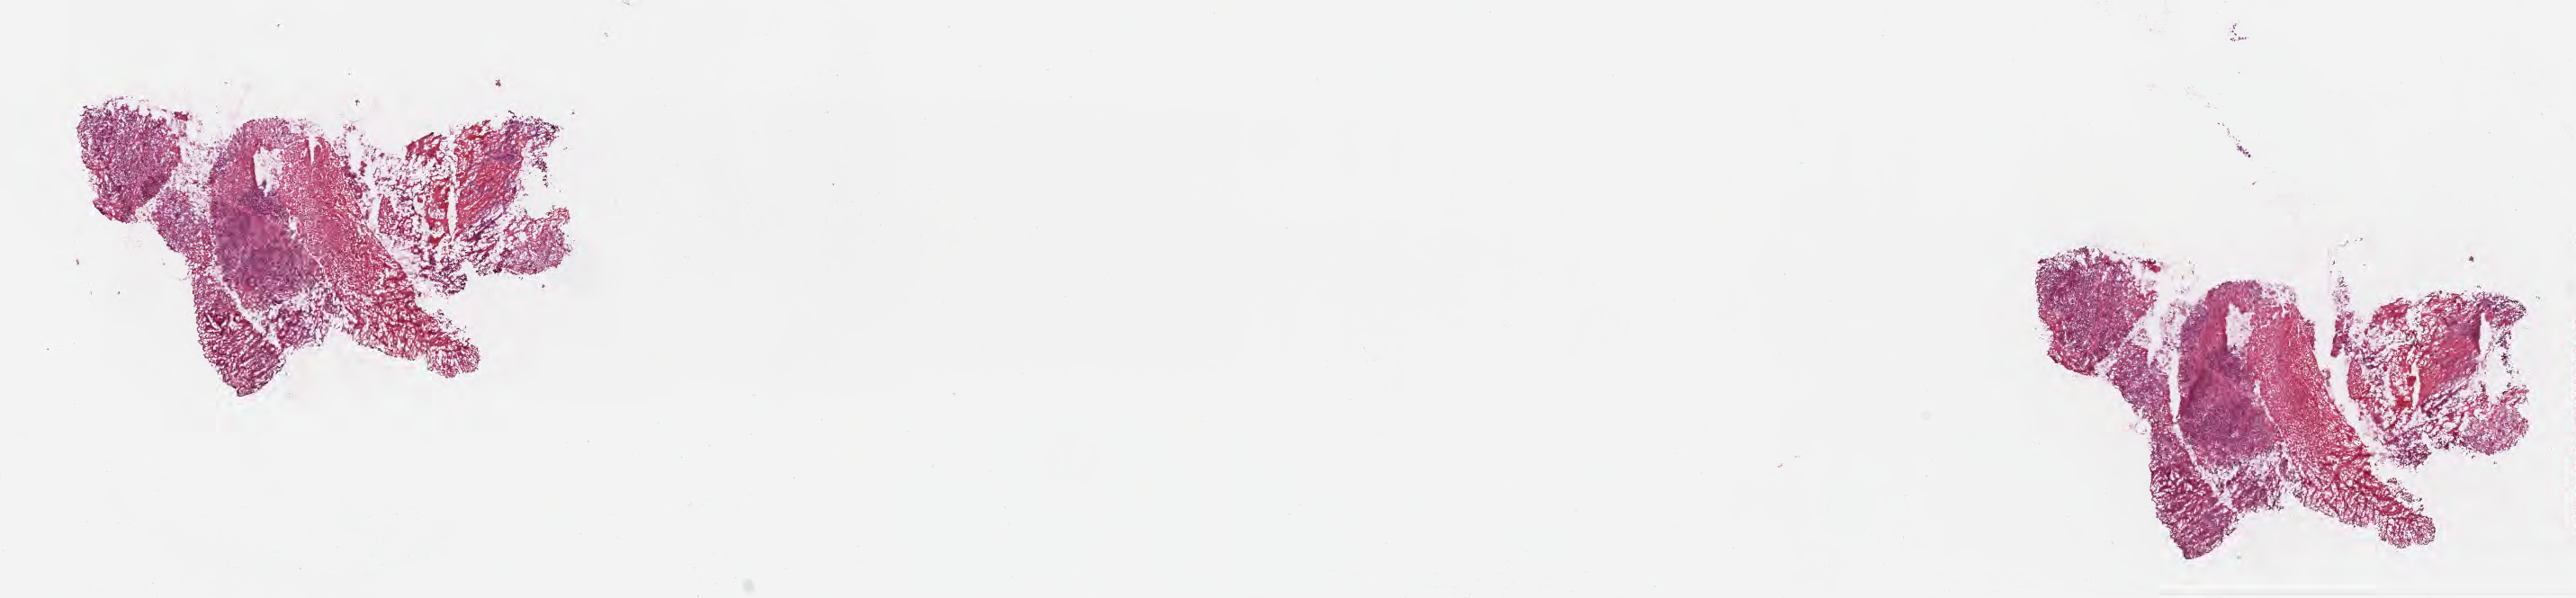
Digitized hematoxylin and eosin (H&E)-stained section — shown as a low-resolution overview of the whole scanned area (about 23.1 x 5.4 mm). Cryosection. Specimen: primary tumor. Anatomic site: splenic flexure of colon. Female patient; age at initial diagnosis 81 years. Tumor grade: G2 (moderately differentiated). Slide review estimates, as recorded: tumor cells 65%, tumor nuclei 65%, stromal cells 15%, necrosis 20%, normal cells 0%. Infiltration values recorded for this section: lymphocyte infiltration 3%, monocyte infiltration 3%, neutrophil infiltration 6%.
• AJCC pathologic stage: Stage IIIC
• diagnosis: Medullary carcinoma, NOS
• section: top of the tissue portion